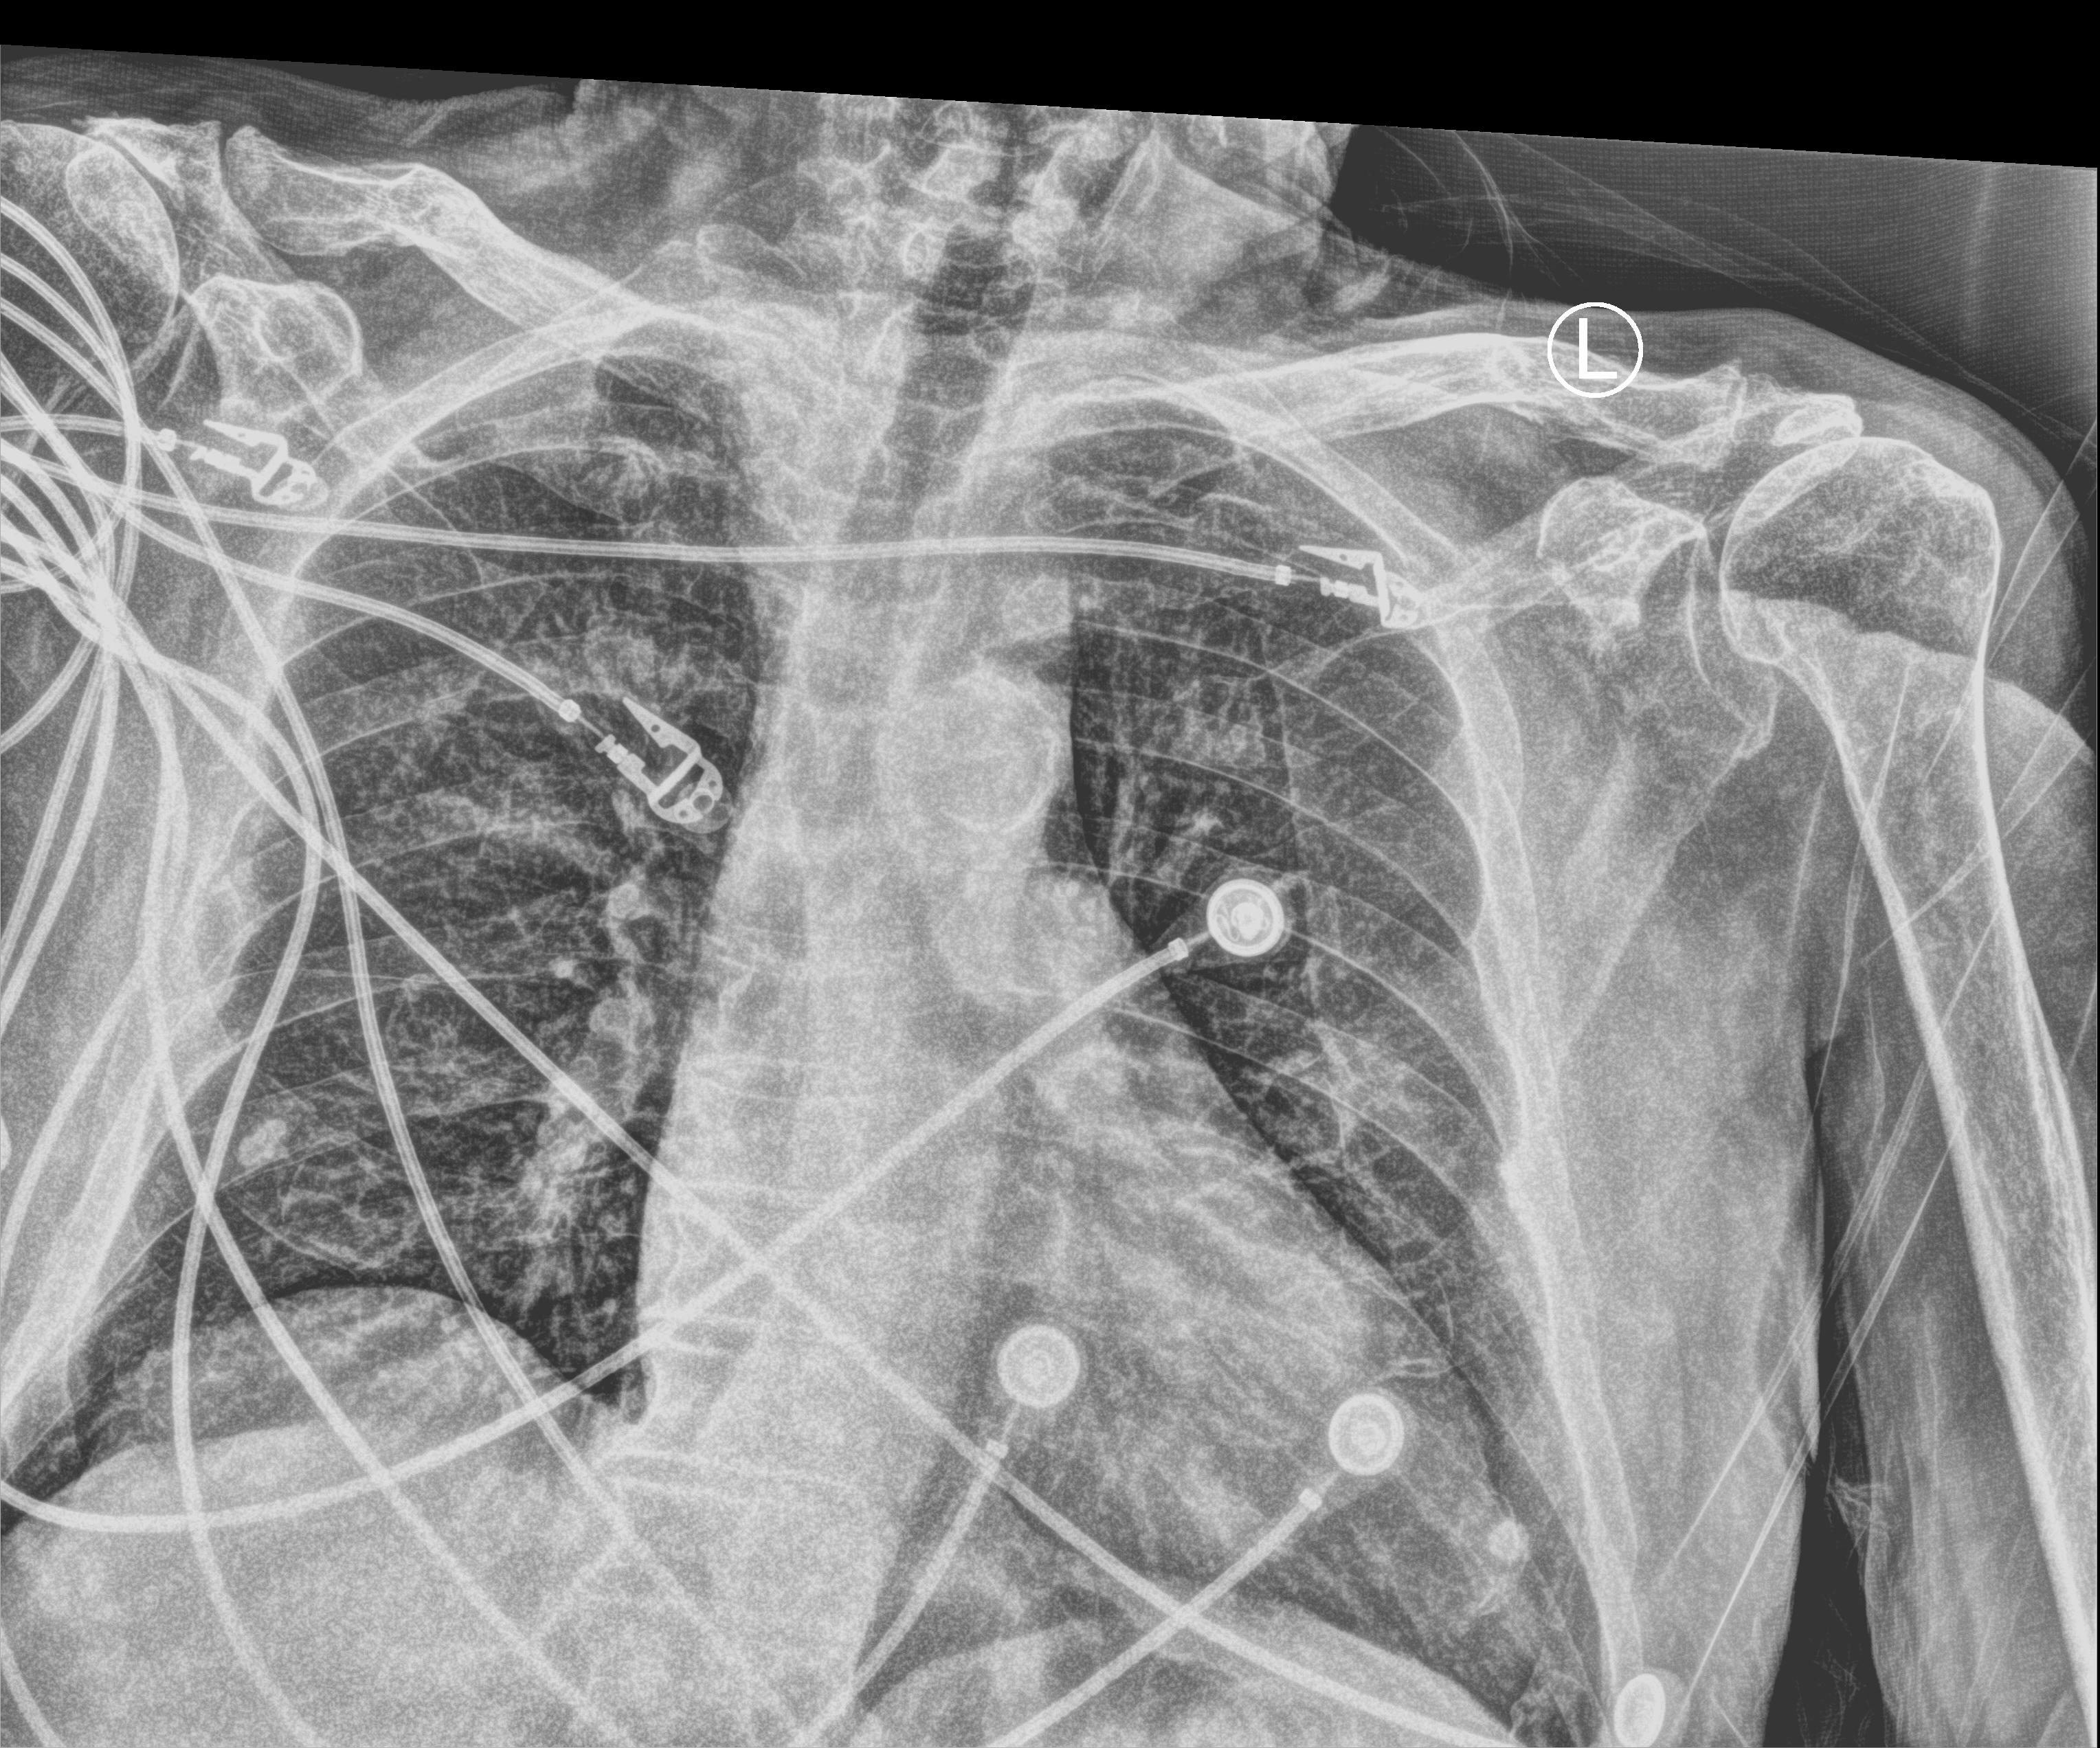
Portable chest radiograph, anteroposterior (AP) projection. Male patient hospitalised with COVID-19, age 75–90 years.
Hospital-stay facts (about this admission, not read from this image; timing relative to this image not recorded):
- mechanically ventilated during this hospital stay: no